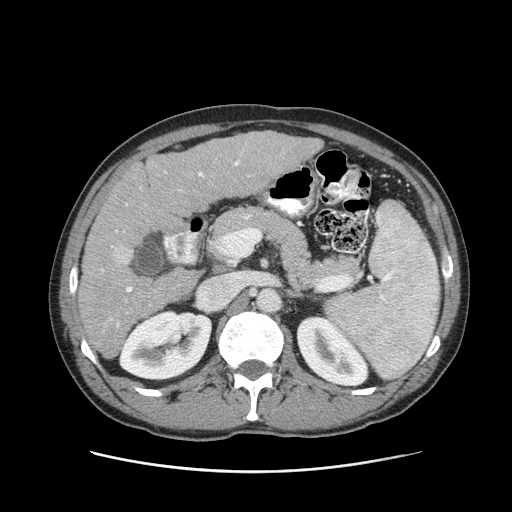
Contrast-enhanced abdominal CT (liver protocol), one axial slice; position 47 of 93 along the scan axis; reconstruction kernel STANDARD; 120 kVp; soft-tissue window (W 400 / L 40 HU); 2.5 mm slice thickness; 512 × 512 image matrix, field of view 380 × 380 mm. Case-level facts recorded for this patient, not image findings: diagnosis: hepatocellular carcinoma (patient treated with transarterial chemoembolisation; whether this scan precedes or follows treatment is not stated here); TNM stage (as recorded): Stage-II; Child-Pugh class: A; tumour differentiation: moderately differentiated; tumour nodularity: multinodular.
Annotated regions visible in this slice (semi-automatically segmented with operator editing):
- liver parenchyma outside the tumour (the mass and vessels are separate outlines, so this box may not span the whole liver): bounding box <78,130,322,358> (left, top, right, bottom; pixels)
- liver vessels: <101,160,240,327>